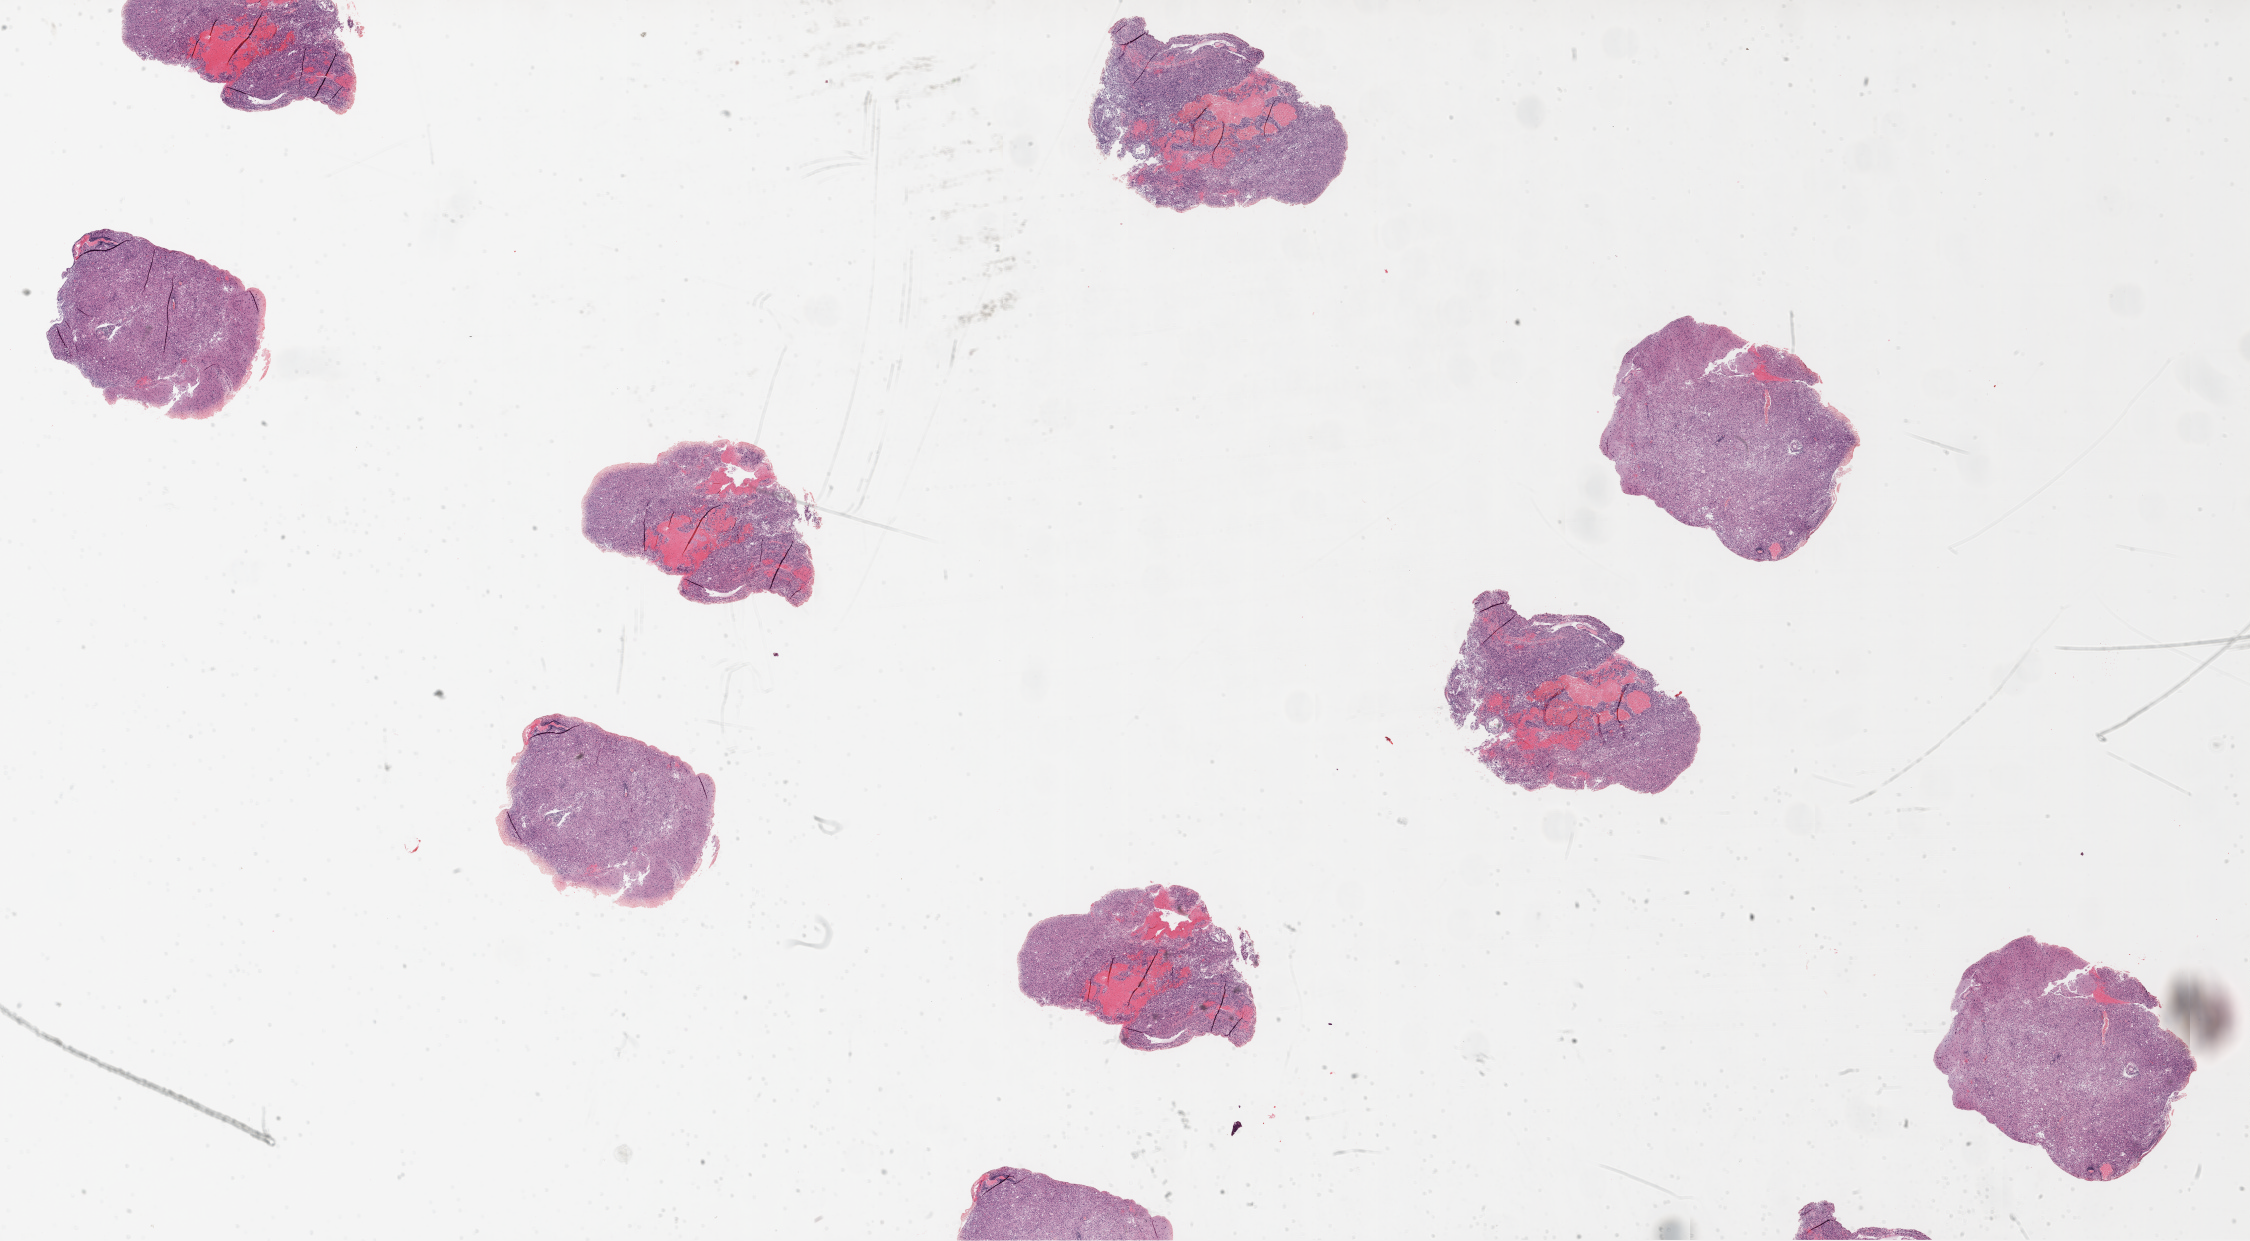
Hematoxylin and eosin (H&E) stained whole-slide image — a low-resolution overview of the entire scanned area, about 36.1 x 19.9 mm (acquisition: 20x scan). FFPE section. Sample: primary tumour, brain. Patient: female, age at initial diagnosis 66 years.
* pathologic diagnosis: Glioblastoma